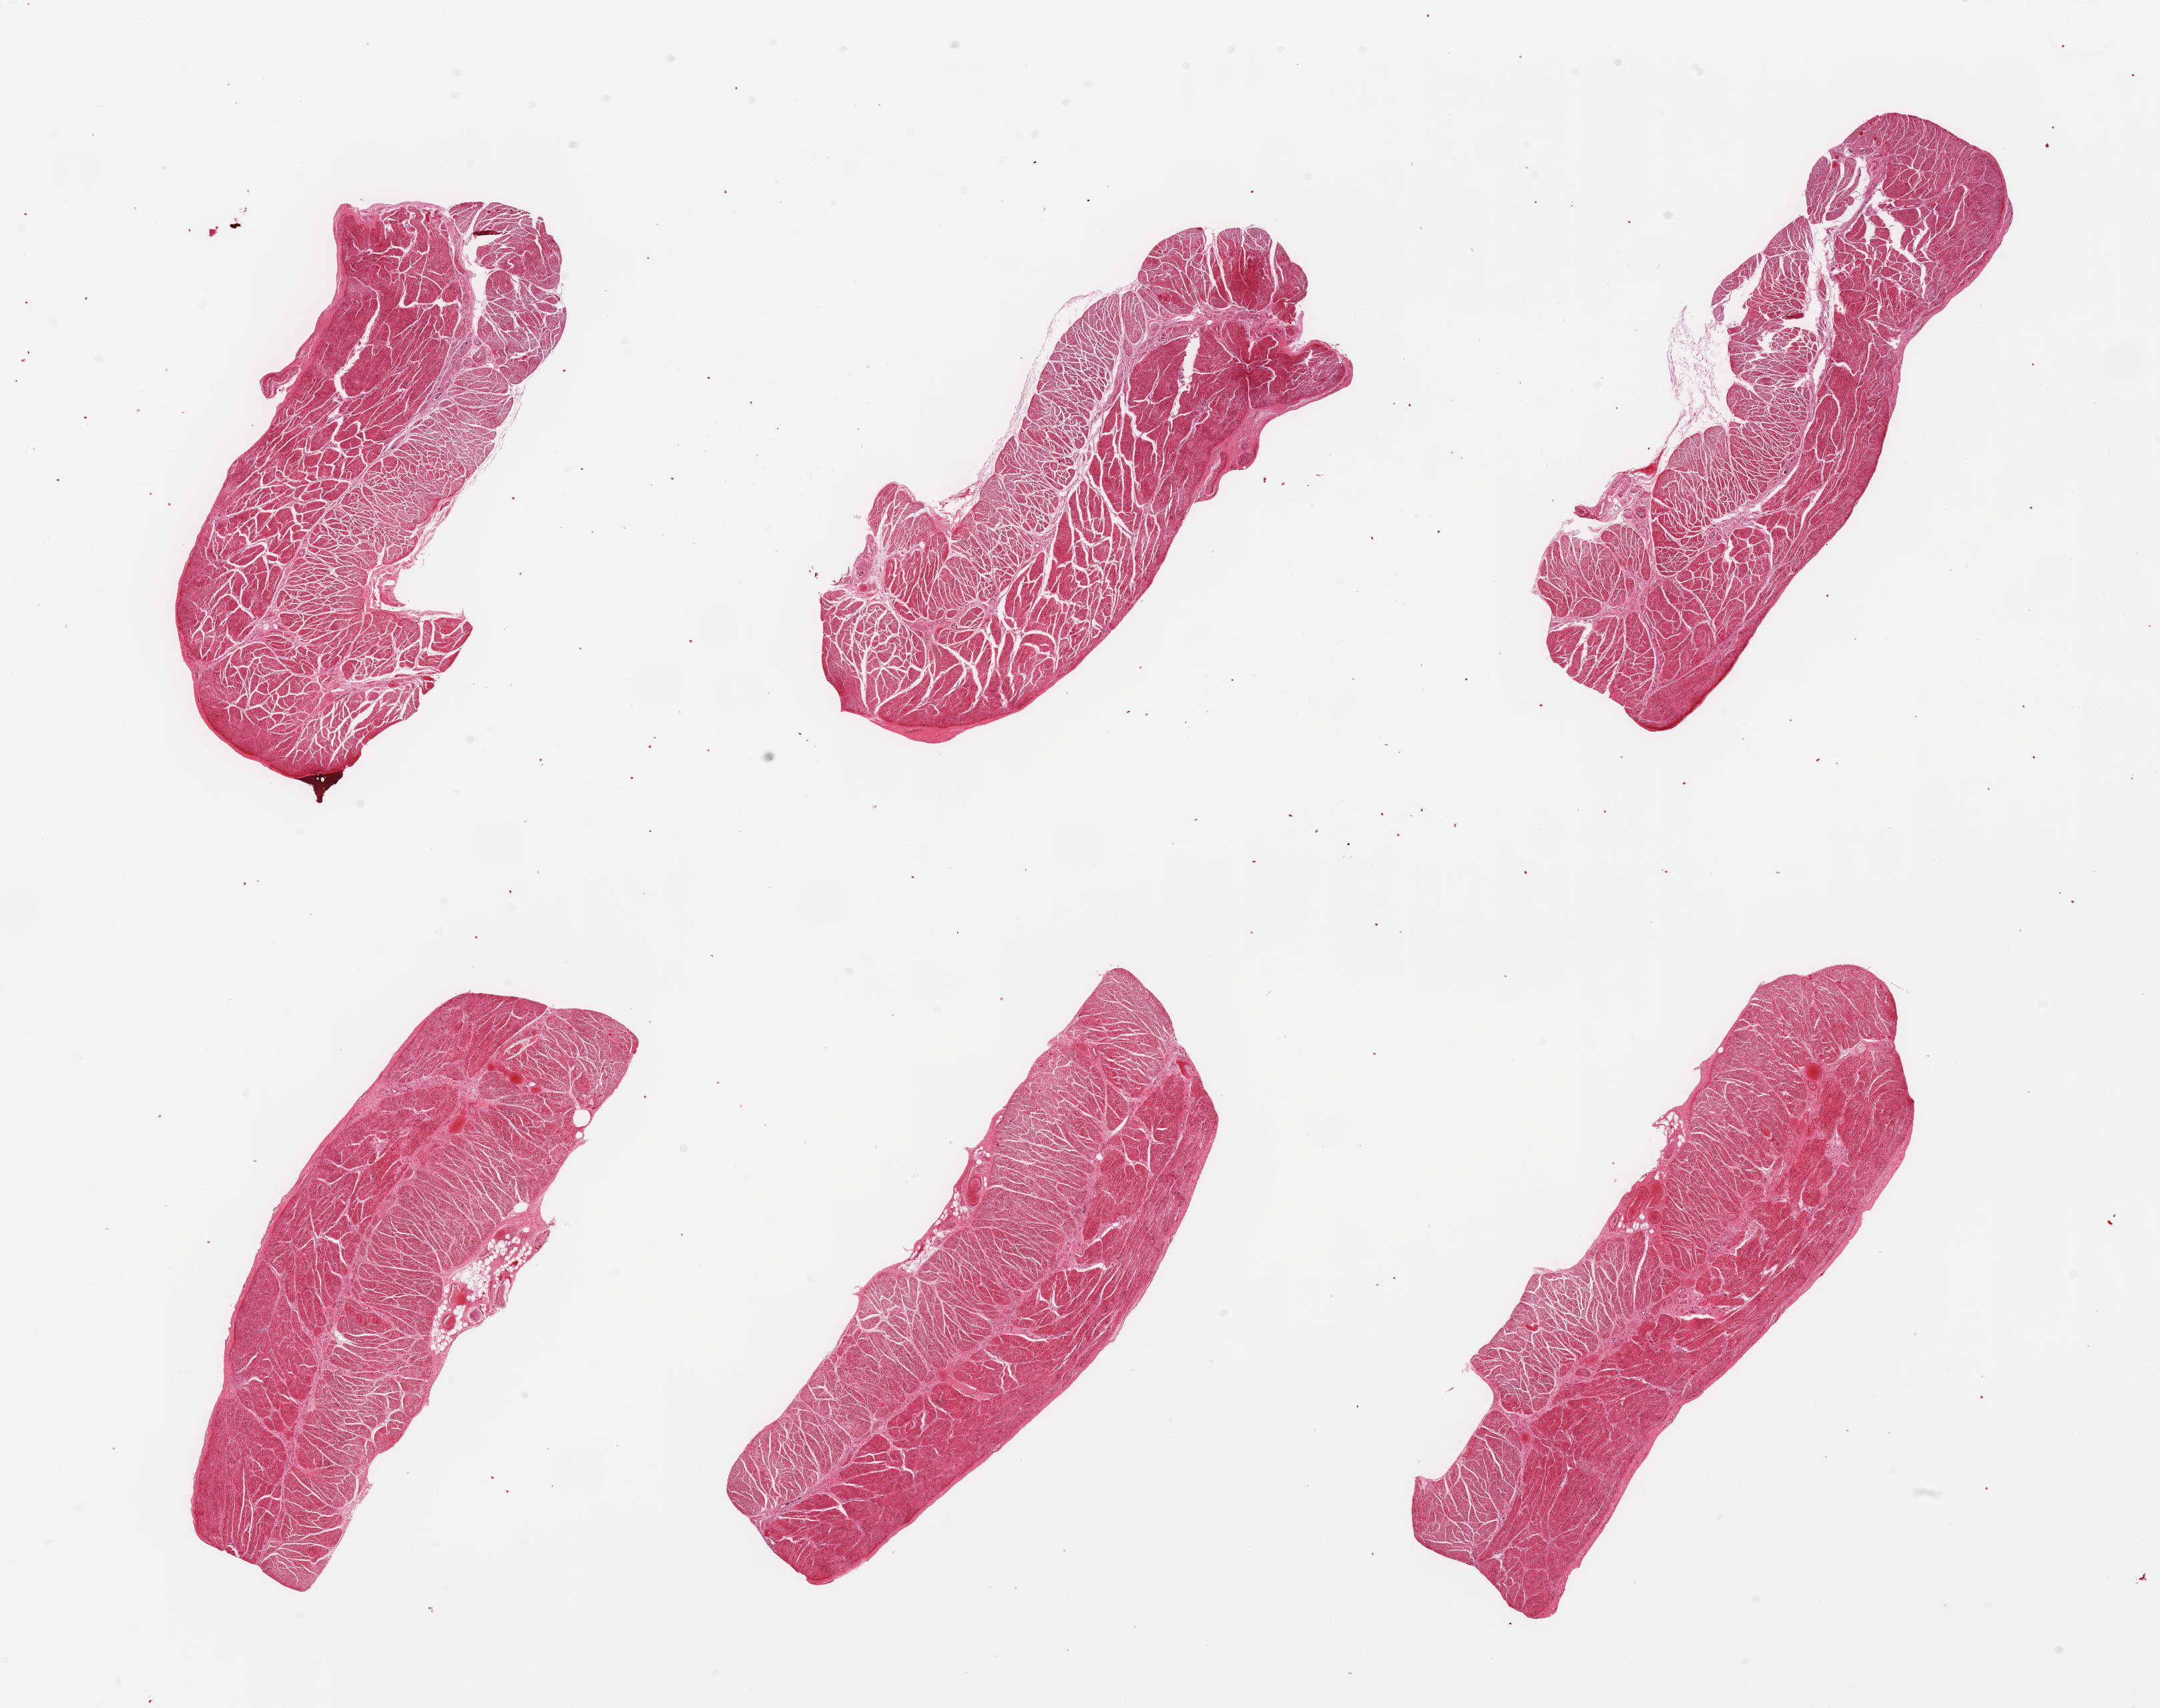
Digitized haematoxylin and eosin-stained section — whole scanned area (about 25.6 x 20.2 mm, slide scanned at 20x) shown as a low-resolution overview. PAXgene-fixed paraffin-embedded (PFPE) section. Sampled site (target tissue): esophageal muscle. Tissue donor sample. Donor sex: male.
Reviewer comment on this tissue sample: 6 pieces; target muscularis.